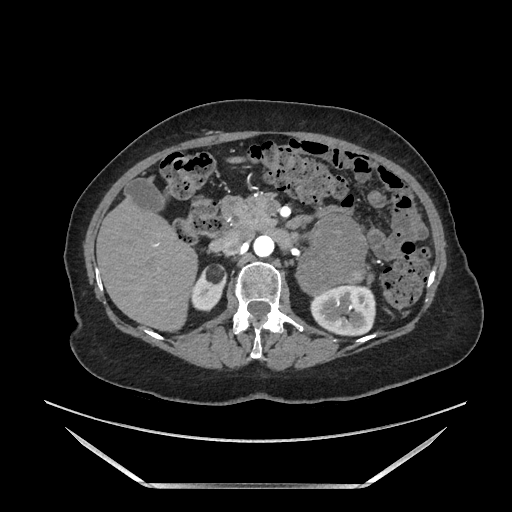
Contrast-enhanced abdominal CT, one axial slice. Position 93 of 205 along the scan axis. Soft-tissue window (W 400 / L 40 HU). 1.25 mm slice thickness. 512 × 512 image matrix, field of view 440 × 440 mm. Female patient. From the clinical record (not read from this slice): diagnosis: adrenocortical carcinoma; tumour side: left adrenal; tumour size at pathology: 12.5 cm; Ki-67 index: 39 %; stage (as recorded): 3.
Annotated regions visible in this slice (semi-automatic segmentation, software-assisted and operator-edited):
- mass: bounding box (x1, y1, x2, y2) in pixels: (299, 217, 364, 294)